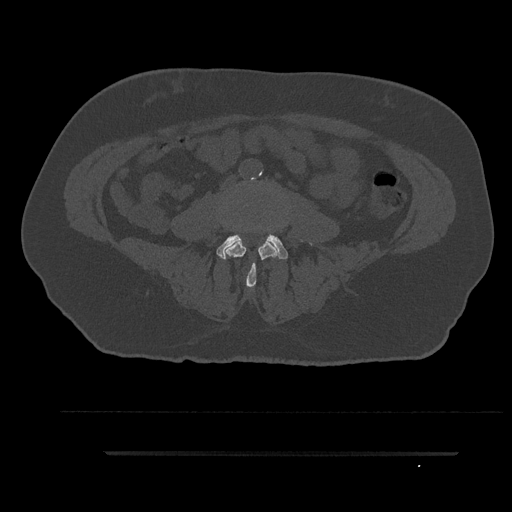
CT including the spine, one axial slice; slice 5 of 797 in the series (ordered by position); 120 kVp; bone window (W 1800 / L 400 HU); 512 × 512 image matrix. Patient: male, 63 years. From the clinical record (not read from this slice): primary cancer: renal; vertebrae with lytic lesions (as recorded): T8.
Annotated regions visible in this slice (semi-automatically segmented with operator editing):
- L3 vertebra: bounding box (x1, y1, x2, y2) in pixels: (225, 240, 278, 287)
- L4 vertebra: (216, 234, 288, 260)